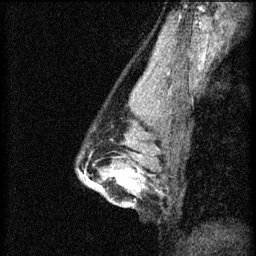
Breast MRI (dynamic contrast-enhanced), one sagittal slice. Position 43 of 60 along the scan axis. 3 images stored at this slice position (order not interpretable as contrast timing). 1.5 T. TE 4.2 ms, TR 8.2 ms. 256 × 256 image matrix, field of view 180 × 180 mm. Patient: female, 44 years.
Outlined on this slice (semi-automatic segmentation, software-assisted and operator-edited):
- analysis volume of interest (the breast-tissue region the enhancement analysis was run in; not a lesion): box from (x=94, y=162) to (x=143, y=205) px
- tumour enhancement mask (voxels above the 70 % enhancement threshold inside the analysis volume of interest): (x=94, y=172)–(x=141, y=191)